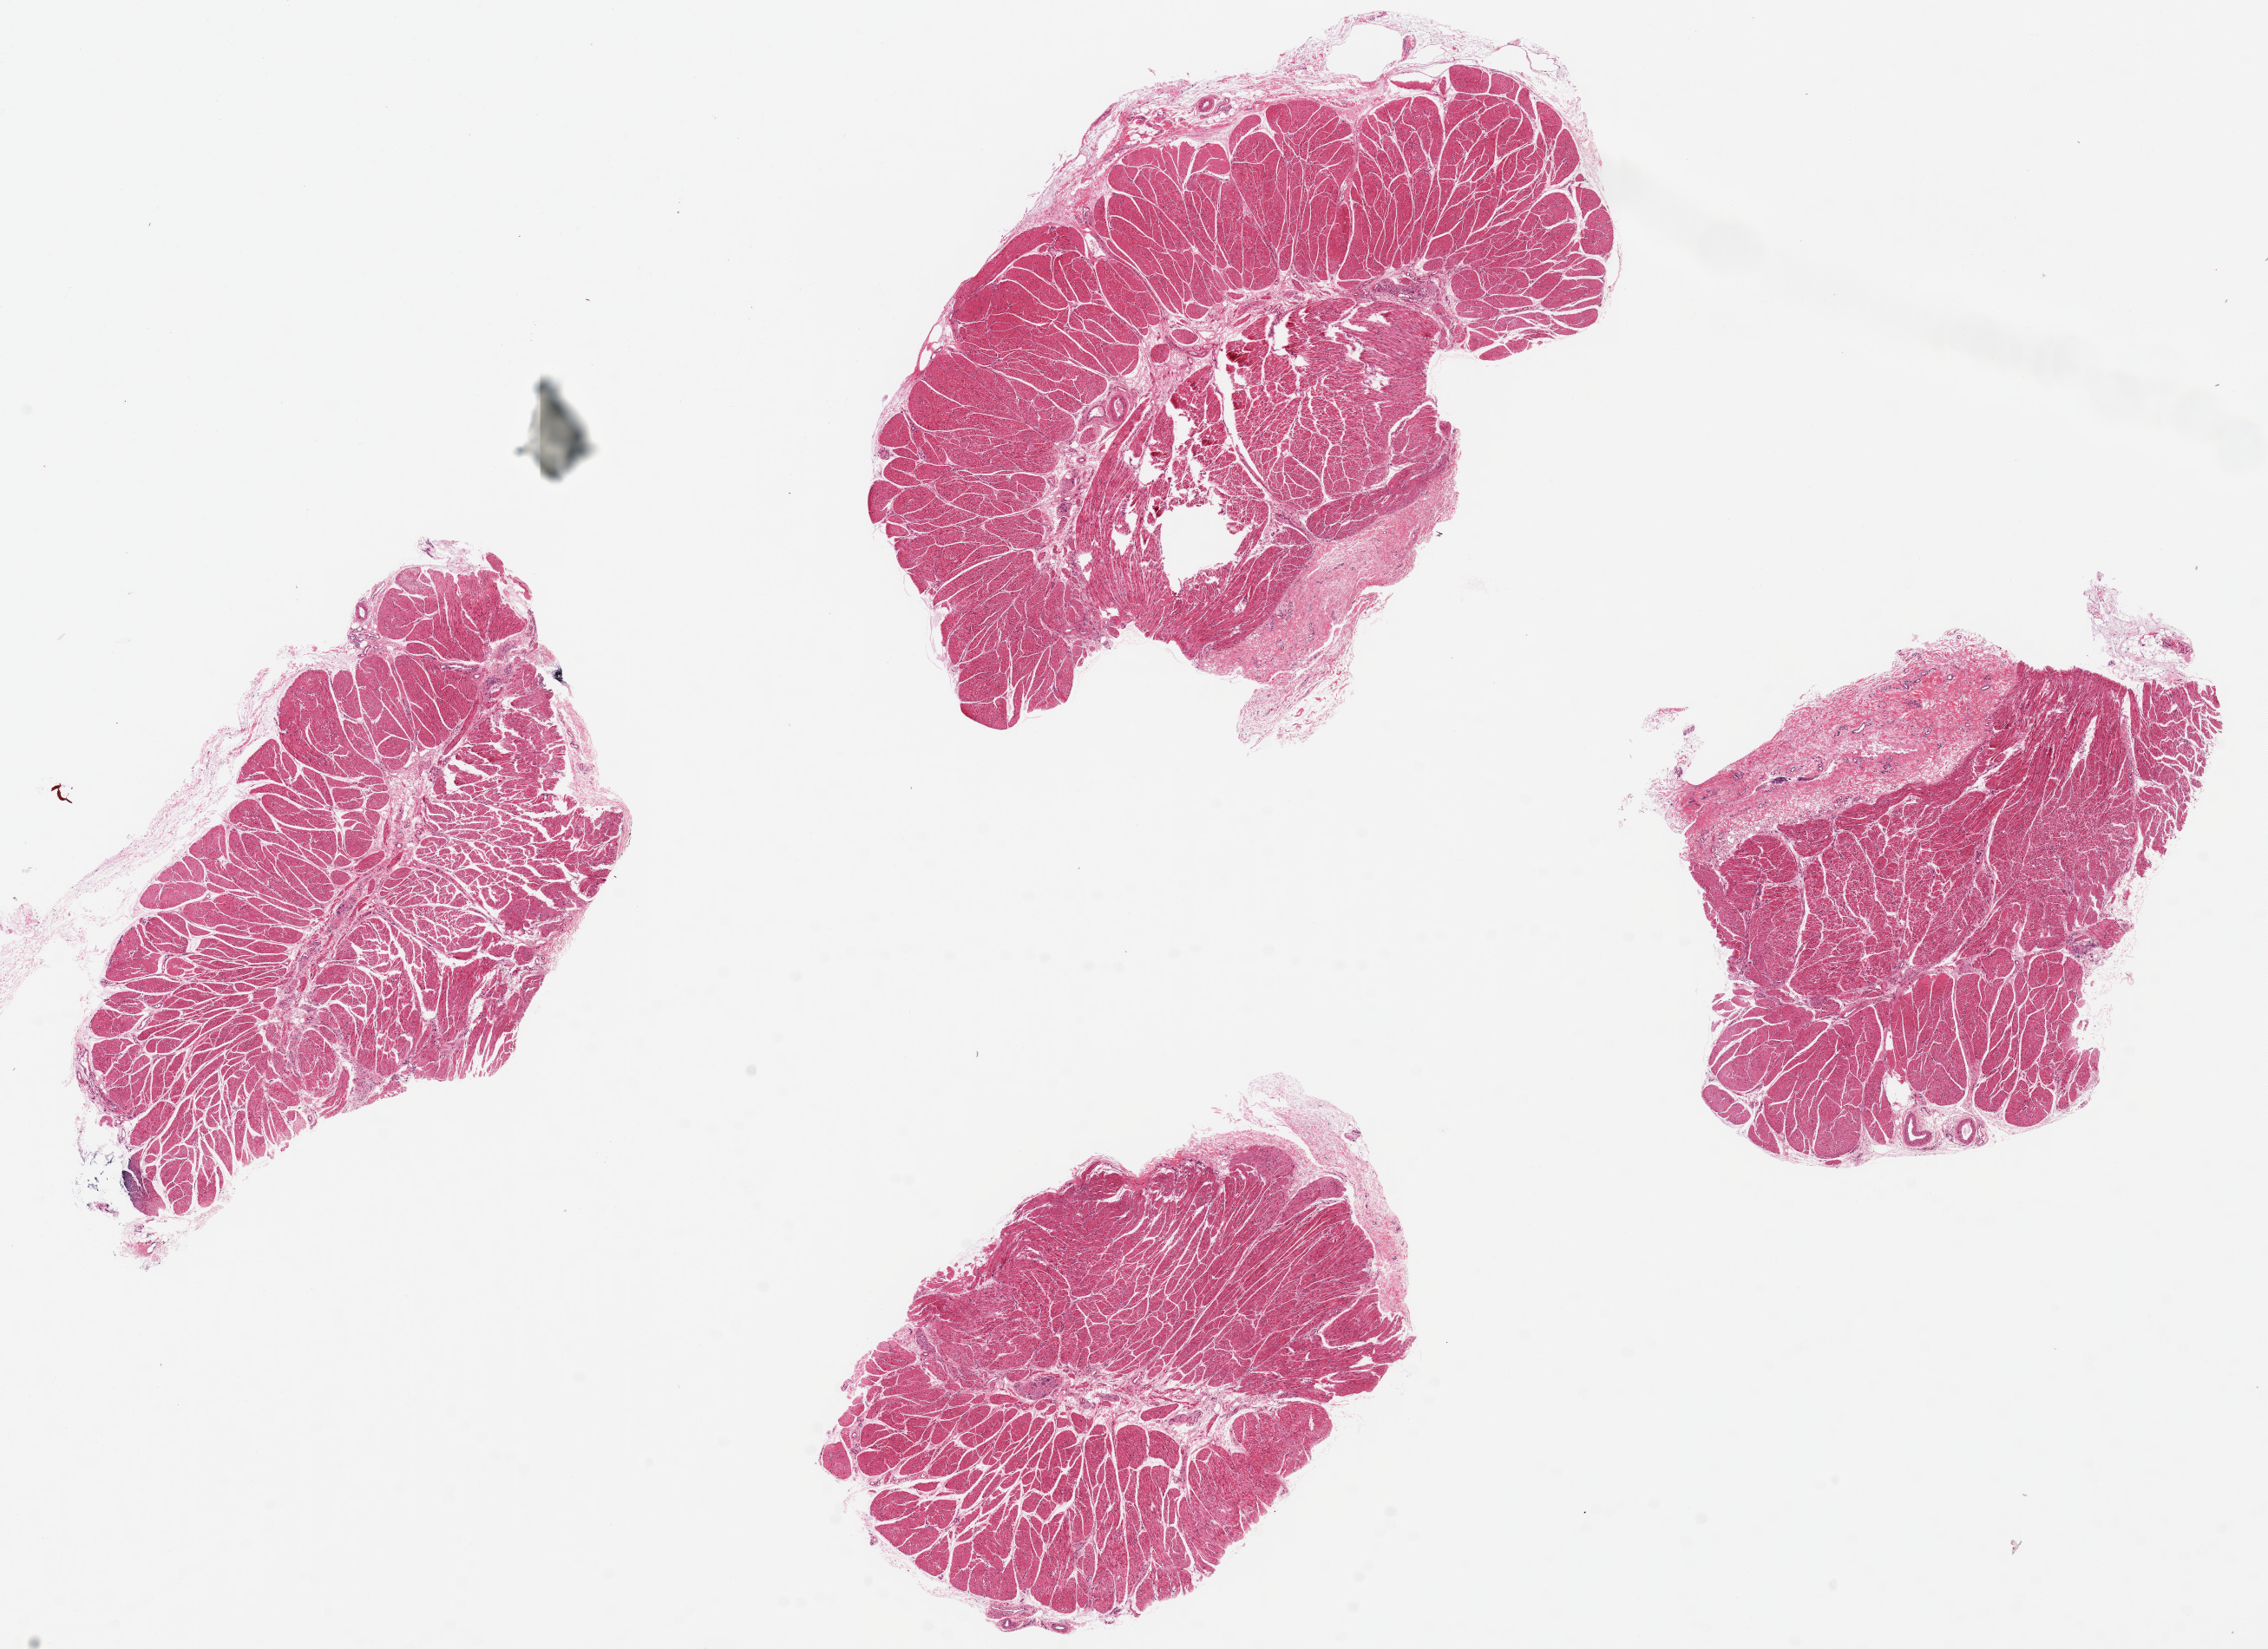
Digitized H&E-stained section, low-resolution overview of the scanned area, about 20.7 x 15.0 mm (slide scanned at 20x), PAXgene-fixed, paraffin-embedded tissue, target tissue: esophageal muscle, donor tissue sample.
Pathologist's review note for this sample: 4 pieces, up to 8x5mm; all muscularis, good specimen.